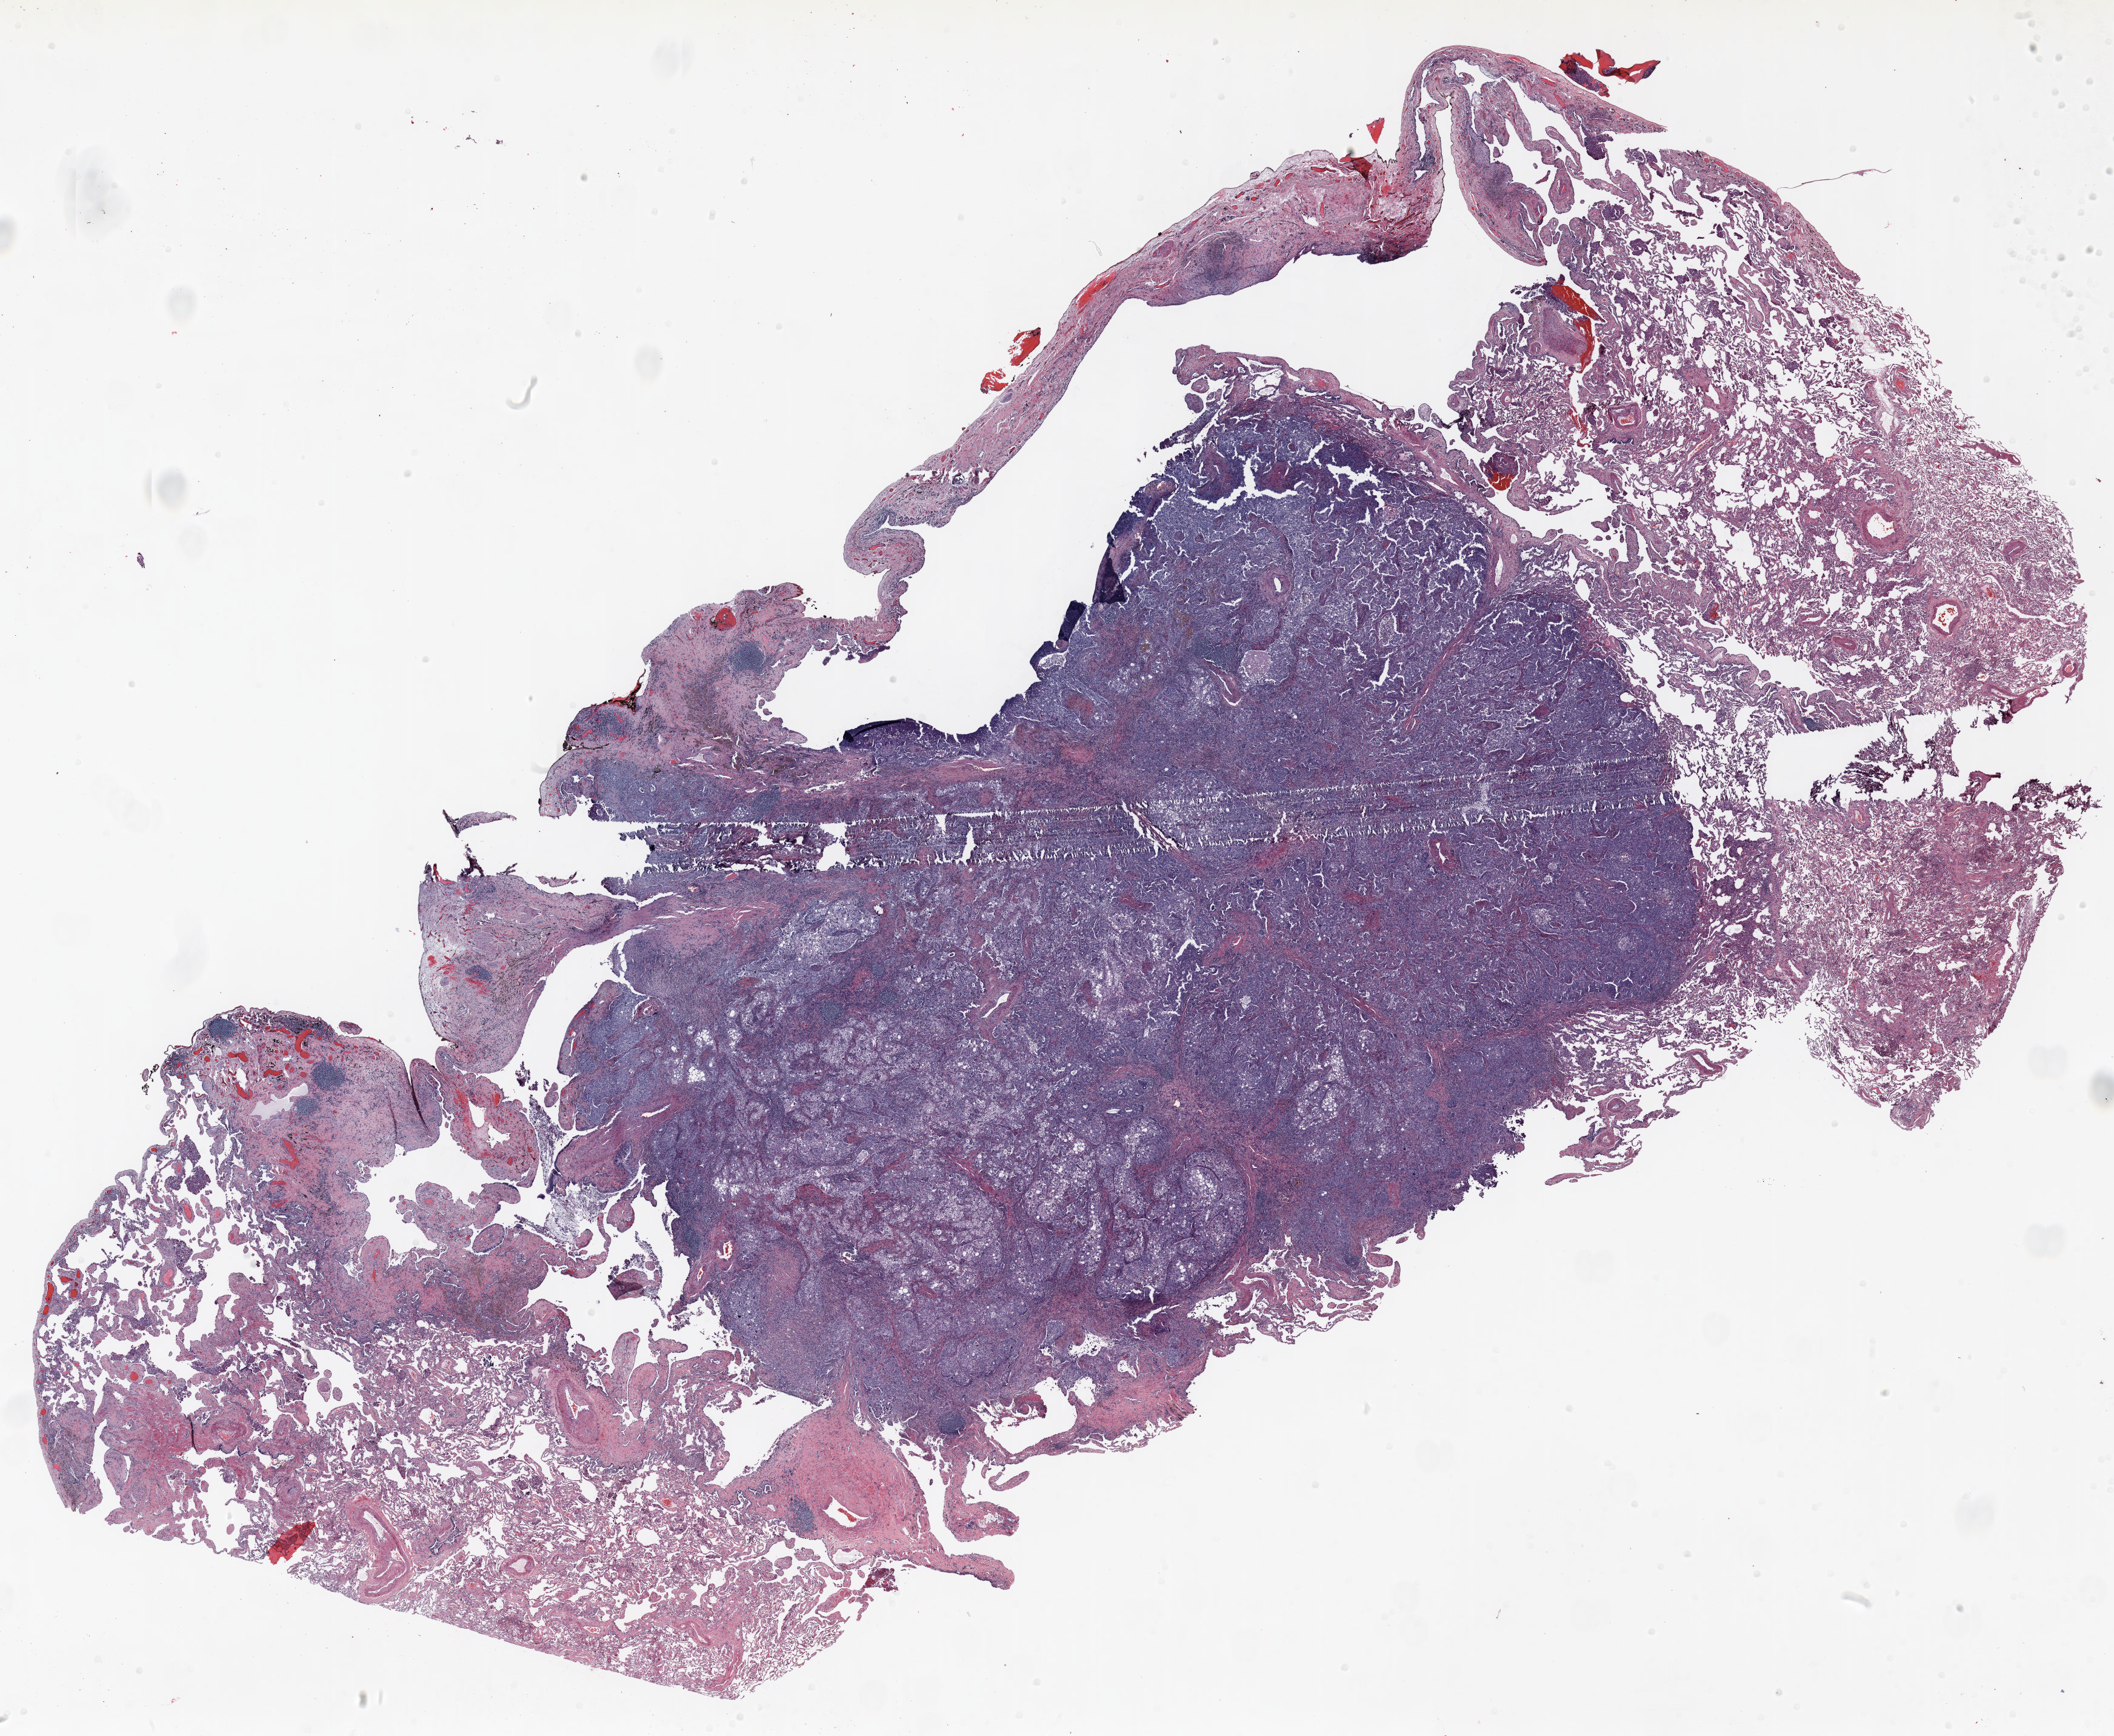
Whole-slide histology image, H&E — whole scanned area (about 28.0 x 23.0 mm, acquisition: 20x scan) shown as a low-resolution overview. Formalin-fixed paraffin-embedded (FFPE) section. Lung tissue. Male patient, aged 62 at enrolment. Current smoker at enrolment.
Participant's lung-cancer diagnosis: Adenocarcinoma, NOS.